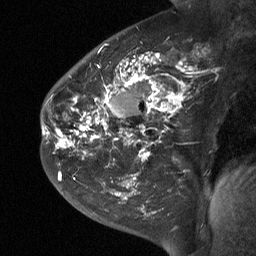
Breast MRI (dynamic contrast-enhanced), one sagittal slice; position 38 of 64 along the scan axis; dynamic contrast-enhanced study with each time point stored as its own series, time point 2 of 3 at this slice position (early post-contrast, ordered by acquisition time); 1.5 T; TE 4.8 ms, TR 27 ms; 2 mm slice thickness; 256 × 256 image matrix. Patient: female, 42 years. From the clinical record (not read from this slice): setting: breast cancer imaged before/during neoadjuvant chemotherapy; receptor status: triple-negative.
Structures marked on this image (semi-automatic segmentation, software-assisted and operator-edited):
- analysis volume of interest (the breast-tissue region the enhancement analysis was run in; not a lesion): bounding box <43,29,200,190> (left, top, right, bottom; pixels)
- tumour enhancement mask (voxels above the 90 % enhancement threshold inside the analysis volume of interest): <43,54,193,181>